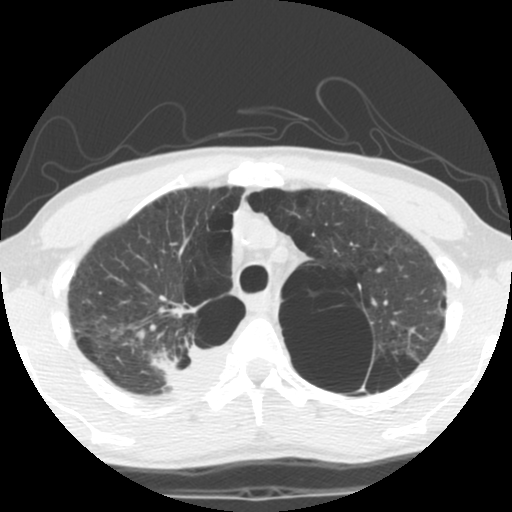
Low-dose screening chest CT, one axial slice; slice 90 of 119 in the series (ordered by position); reconstruction kernel STANDARD; 140 kVp; lung window (W 1500 / L -600 HU); 512 × 512 image matrix, field of view 295 × 295 mm.
Annotated regions visible in this slice (outlined manually by an expert reader):
- lesion 1 (tumor, upper lobe of right lung): bounding box <151,348,226,393> (left, top, right, bottom; pixels)